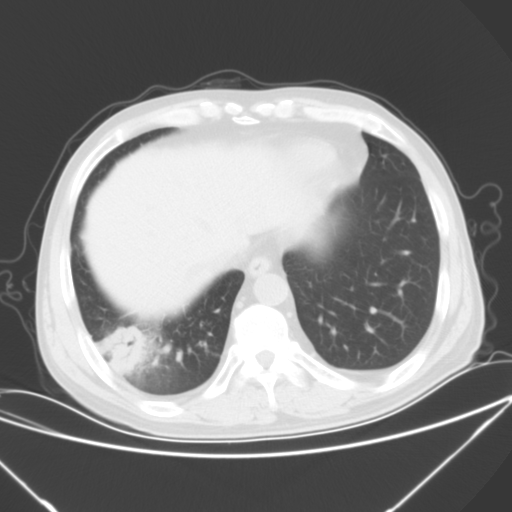
Chest CT, one axial slice. Slice 17 of 57 in the series (ordered by position). Lung window (W 1500 / L -600 HU). 5 mm slice thickness. 512 × 512 image matrix. Patient: male, 54 years. From the clinical record (not read from this slice): clinical TNM (as recorded): T2 N1 M0; histopathological grade: G3.
Outlined on this slice (rectangle marked by the reading radiologist):
- lung tumour (recorded histology: adenocarcinoma): bounding box <99,326,144,376> (left, top, right, bottom; pixels)